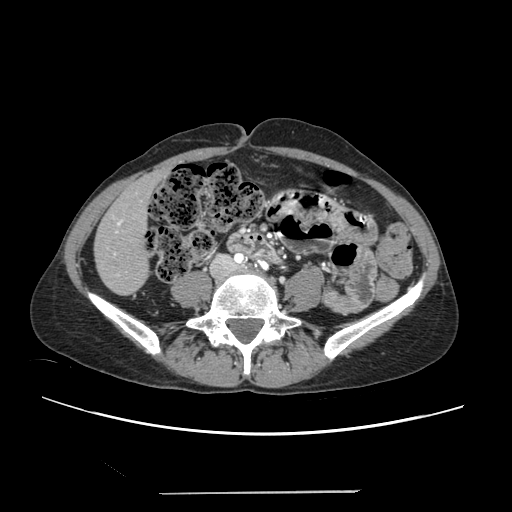
Contrast-enhanced abdominal CT, one axial slice; position 40 of 240 along the scan axis; 120 kVp; intravenous contrast given; soft-tissue window (W 400 / L 40 HU); 512 × 512 image matrix, field of view 371 × 371 mm. Female patient, age 60 years. From the clinical record (not read from this slice): diagnosis: colorectal cancer liver metastases, imaged before liver resection; multiple liver metastases: no; largest metastasis: 1.5 cm.
Outlined on this slice (expert manual segmentation):
- liver: box from (x=95, y=173) to (x=162, y=294) px
- planned liver remnant (the part of the liver to remain after resection): (x=95, y=173)–(x=163, y=294)
- portal vein (with intrahepatic branches): (x=114, y=218)–(x=122, y=275)